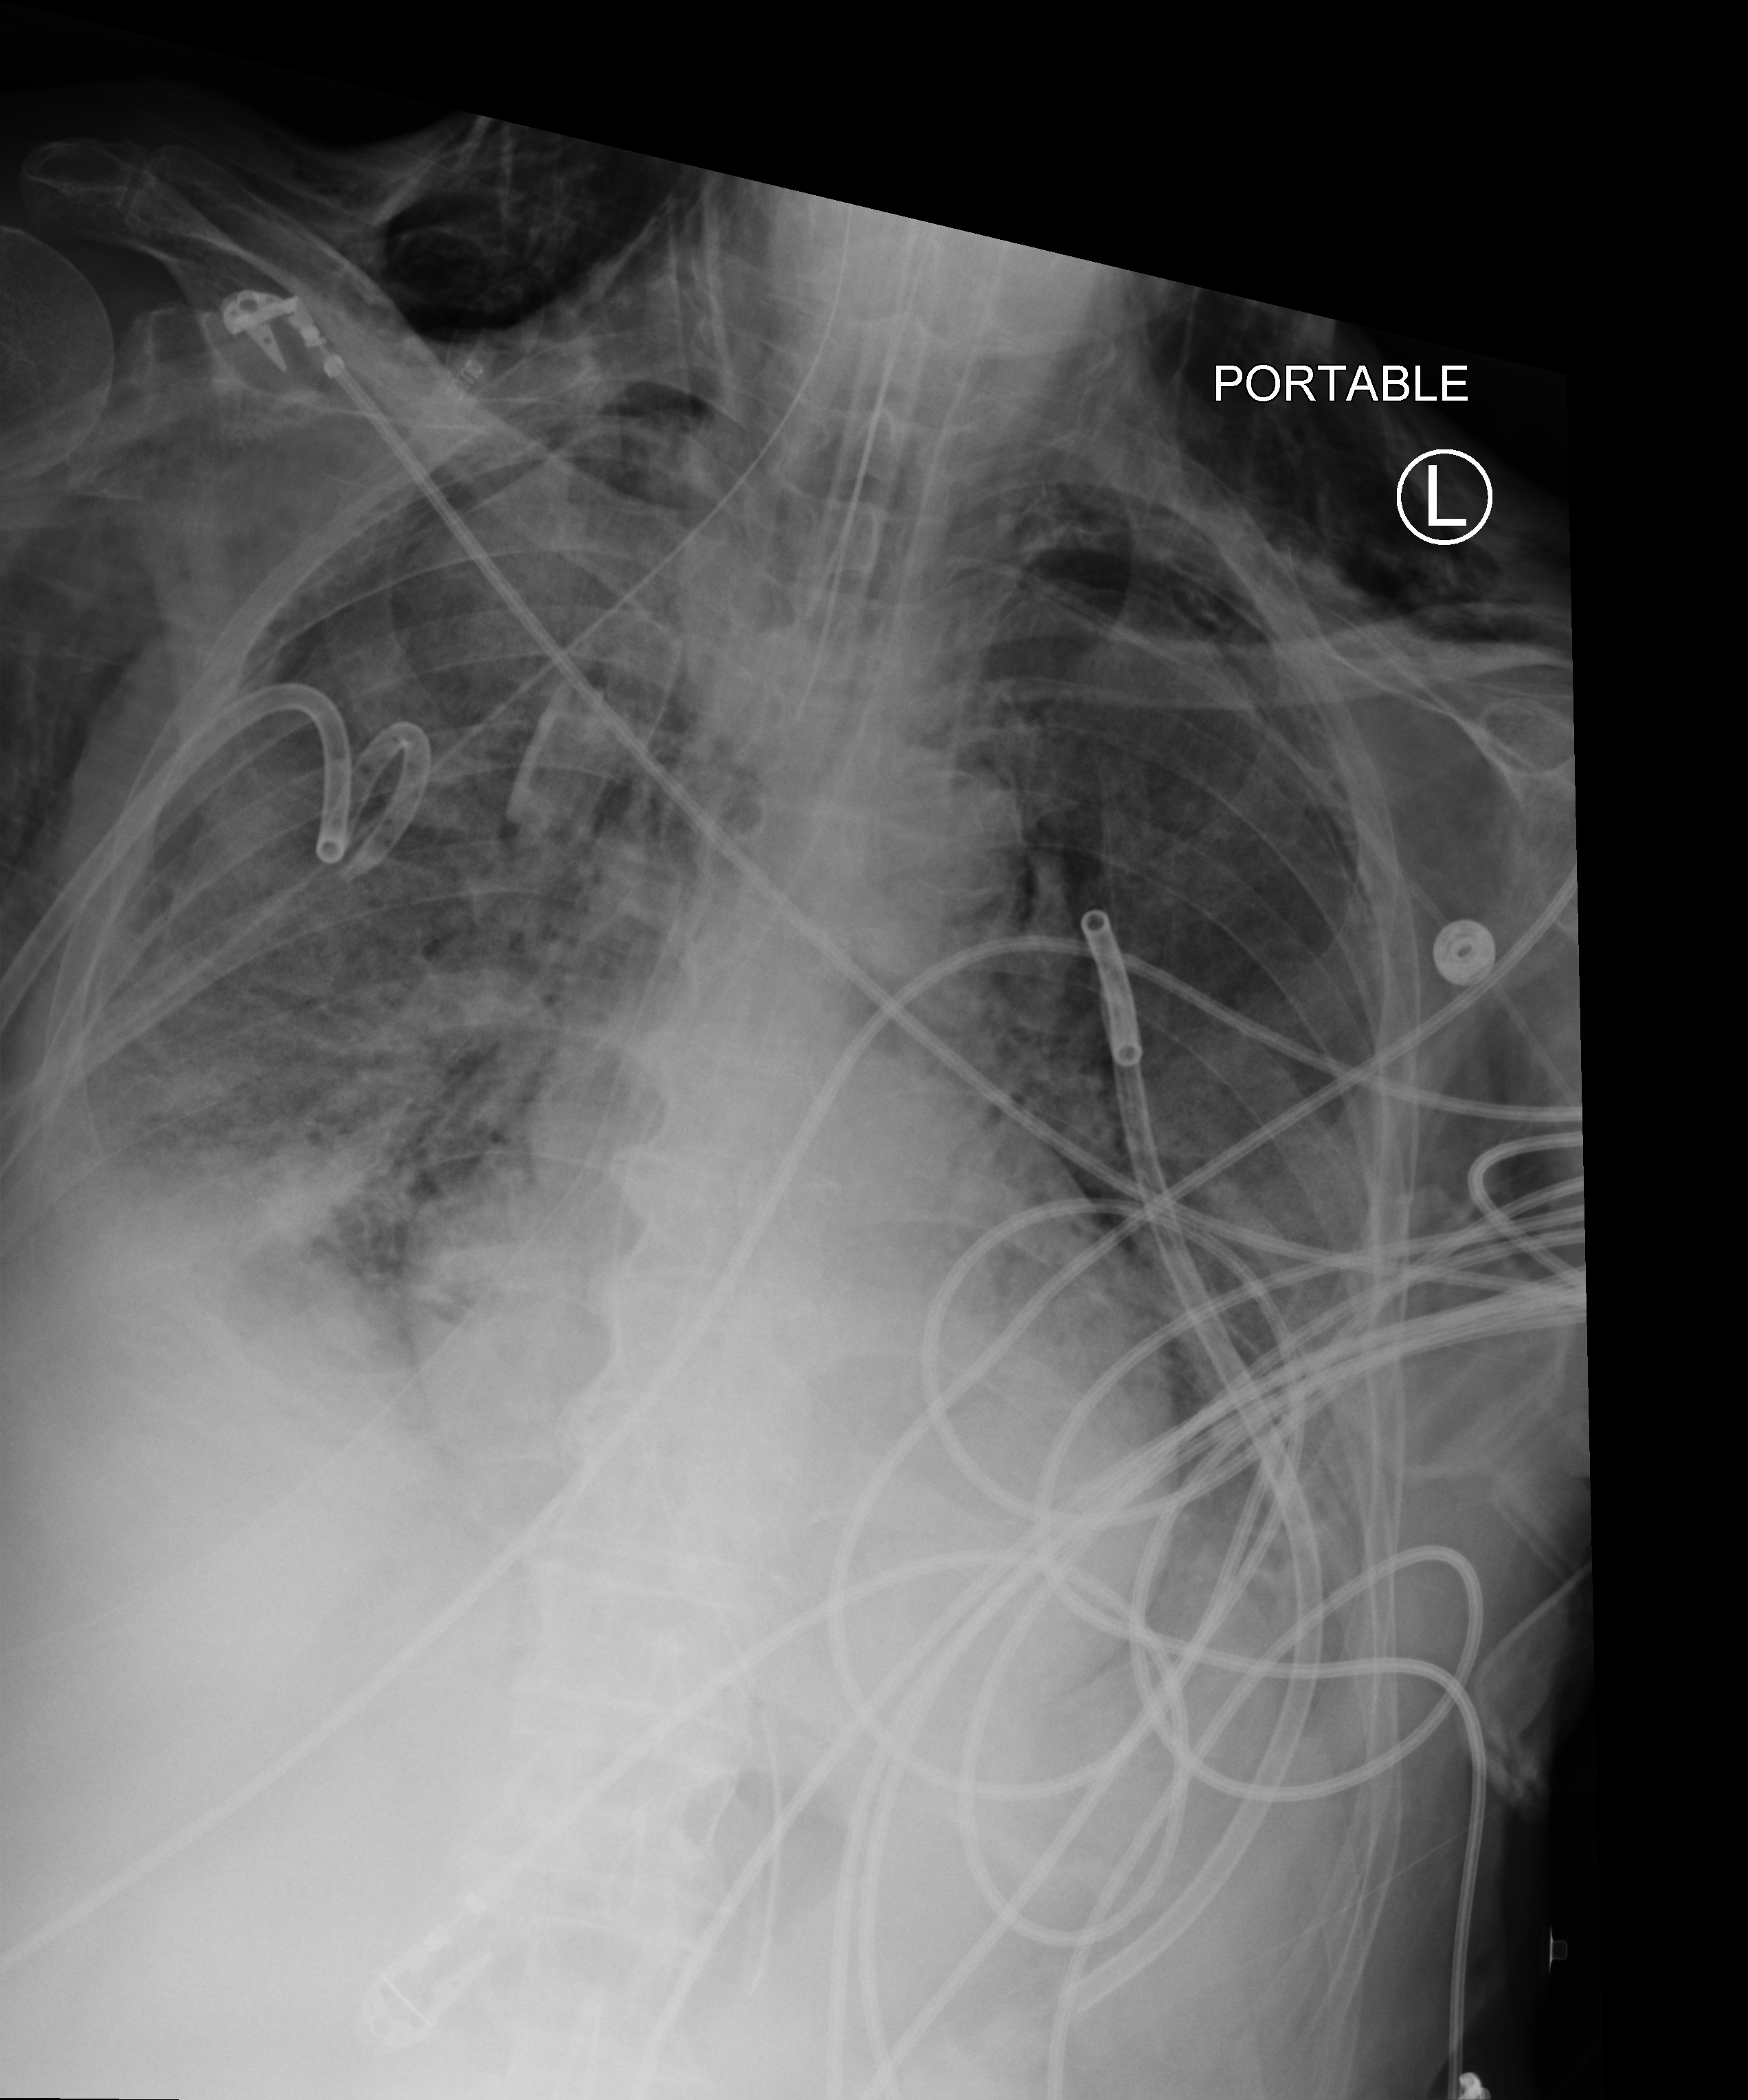
Bedside chest radiograph (computed radiography), anteroposterior (AP) projection. Male patient hospitalised with COVID-19, age 75–90 years.
From the hospital-stay record, not from the radiograph (when in the stay this image was taken is not recorded):
- diabetes (admission record): no
- admitted to intensive care during this hospital stay: yes
- hypertension (admission record): yes